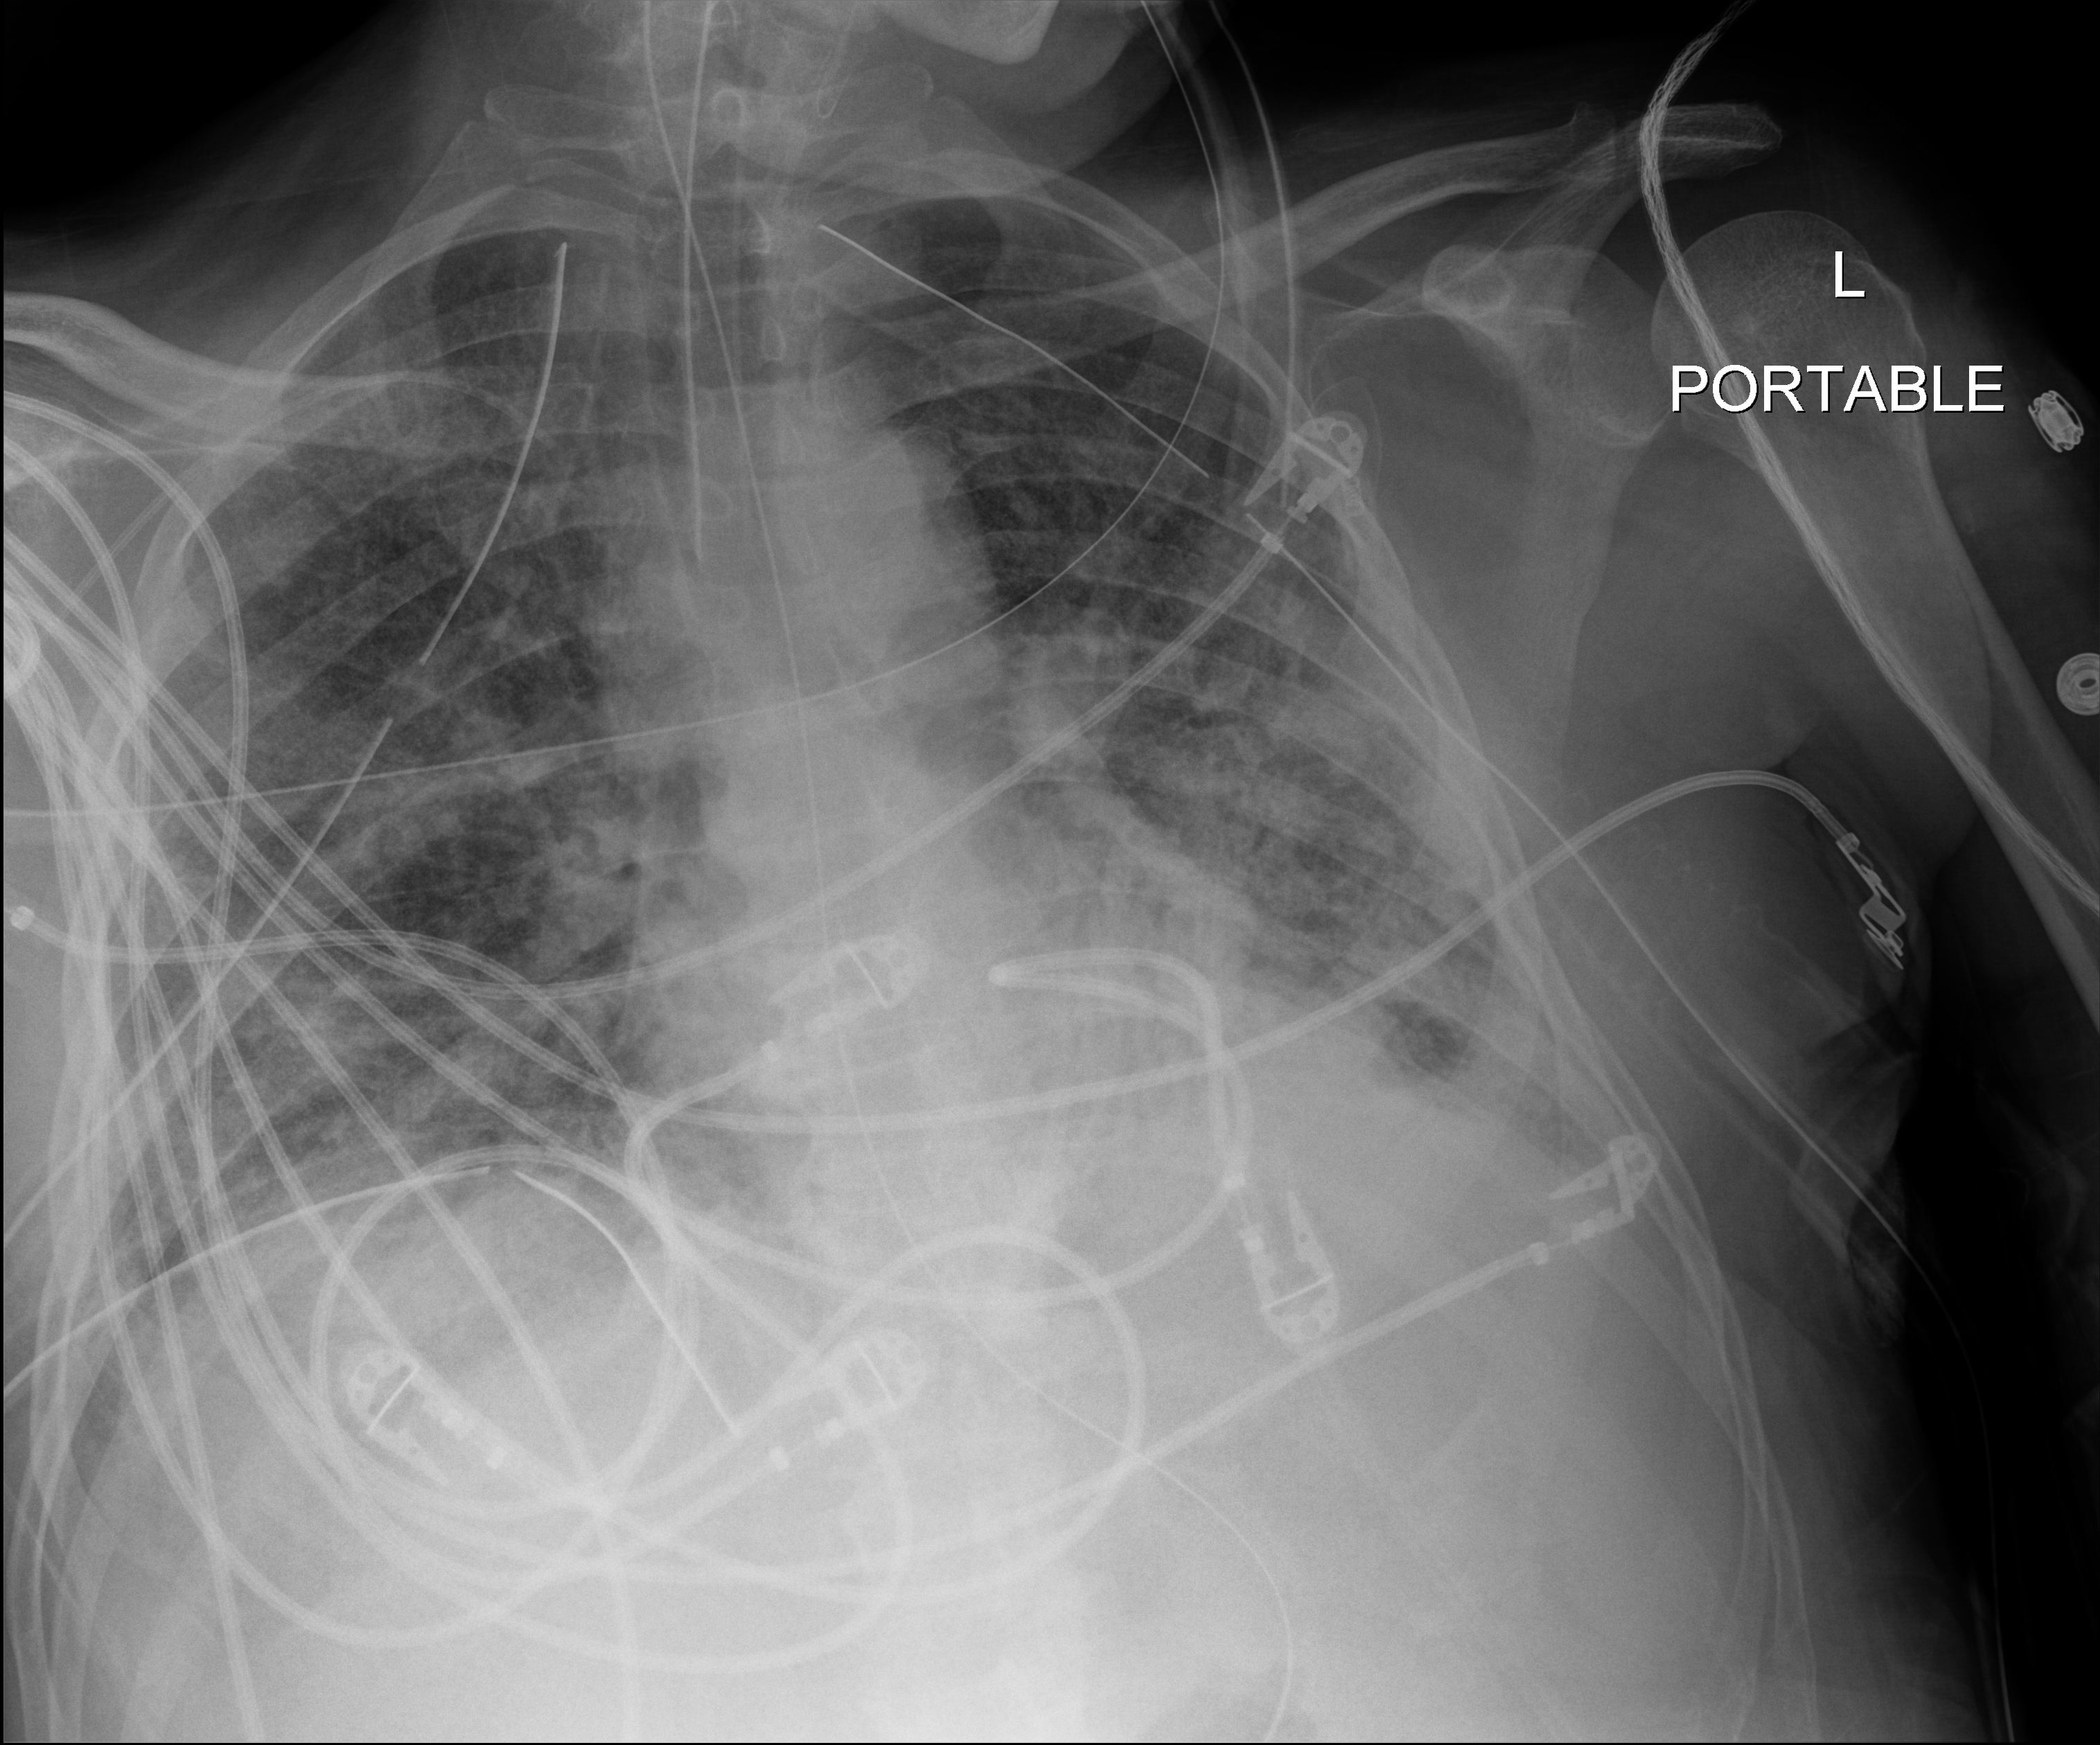
Bedside chest radiograph (digital radiography), anteroposterior (AP) projection. Patient hospitalised with COVID-19; male, aged 18–59 years.
From the hospital-stay record, not from the radiograph (when in the stay this image was taken is not recorded): COPD (admission record): no; length of hospital stay: 83 days.